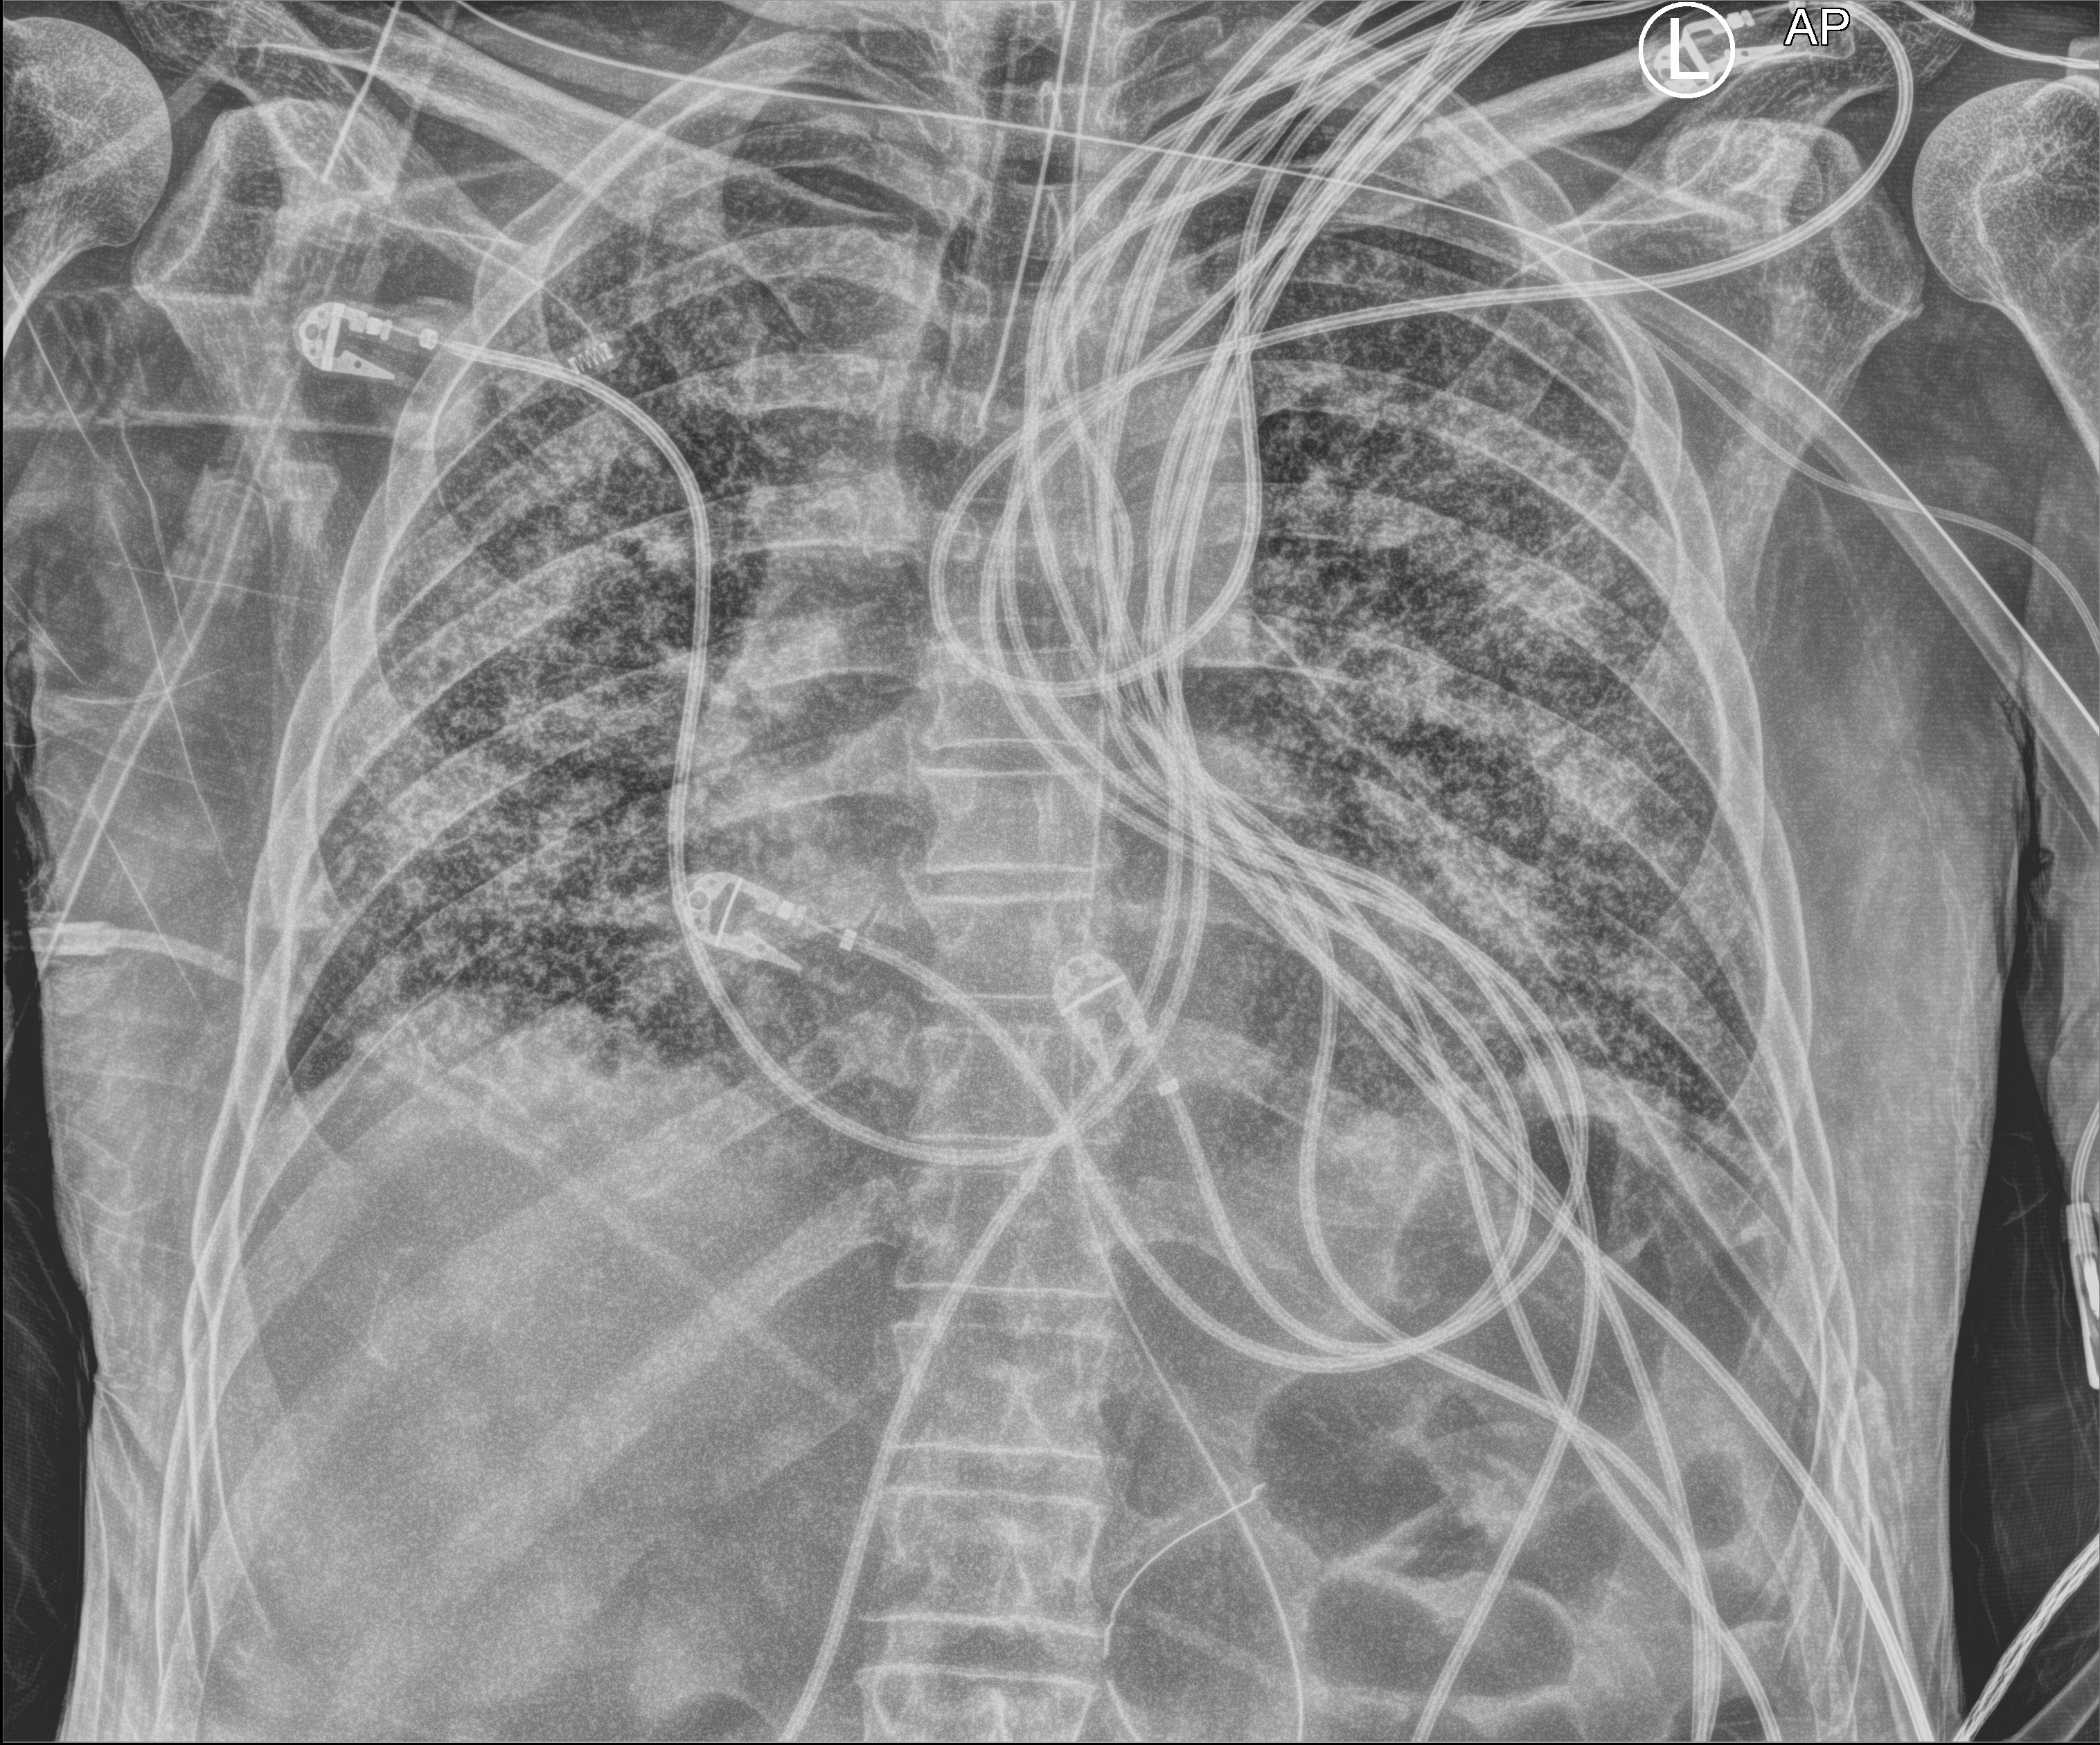
Bedside chest radiograph (computed radiography); anteroposterior (AP) projection. Male patient hospitalised with COVID-19, age 60–74 years.
Hospital-stay facts (about this admission, not read from this image; timing relative to this image not recorded): mechanically ventilated during this hospital stay: yes; length of hospital stay: 54 days.